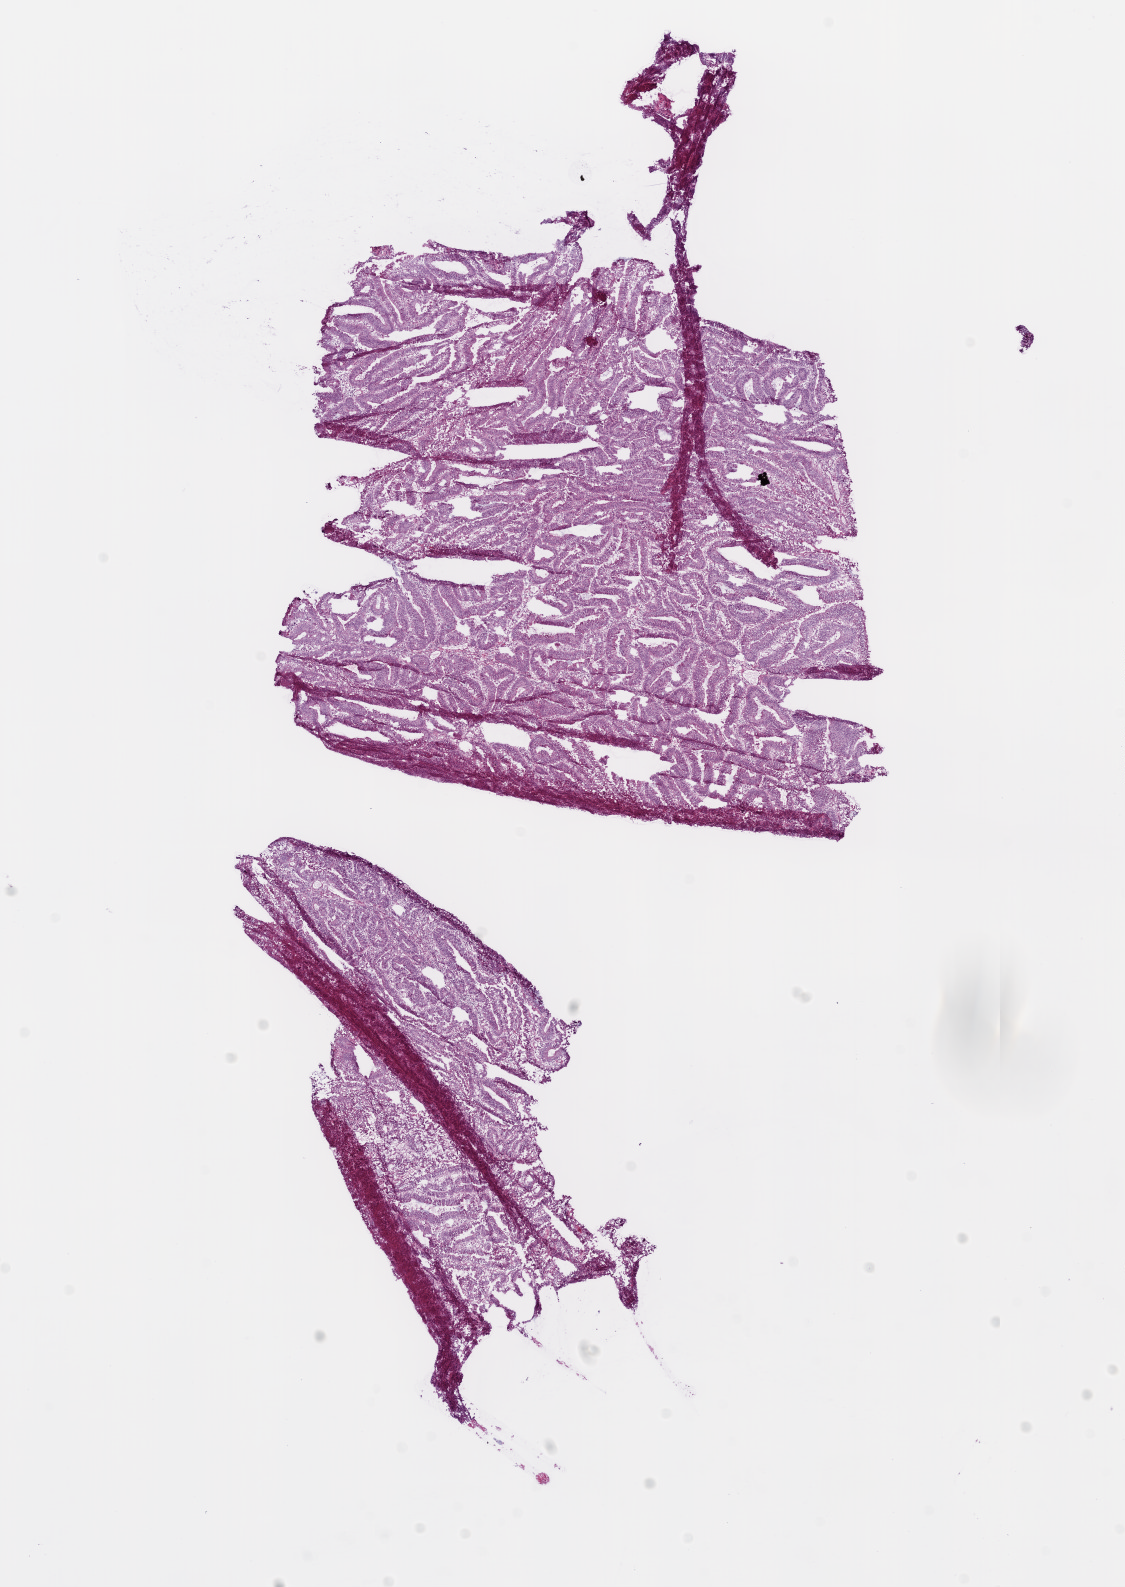
Digitized H&E-stained tissue section (whole slide), a low-resolution overview of the entire scanned area, about 9.0 x 12.7 mm (slide scanned at 20x). Frozen section from the top of the tissue portion. Primary tumour sample from the colon. Female, age 78 years at initial diagnosis. Pathologist review of this section (percent, as recorded): tumour cells 80%, tumour nuclei 85%, normal cells 0%, stromal cells 10%, necrosis 10%.
TNM: T3 N2 M0. Histologic diagnosis: Adenocarcinoma, NOS. AJCC pathologic stage: IIIC.